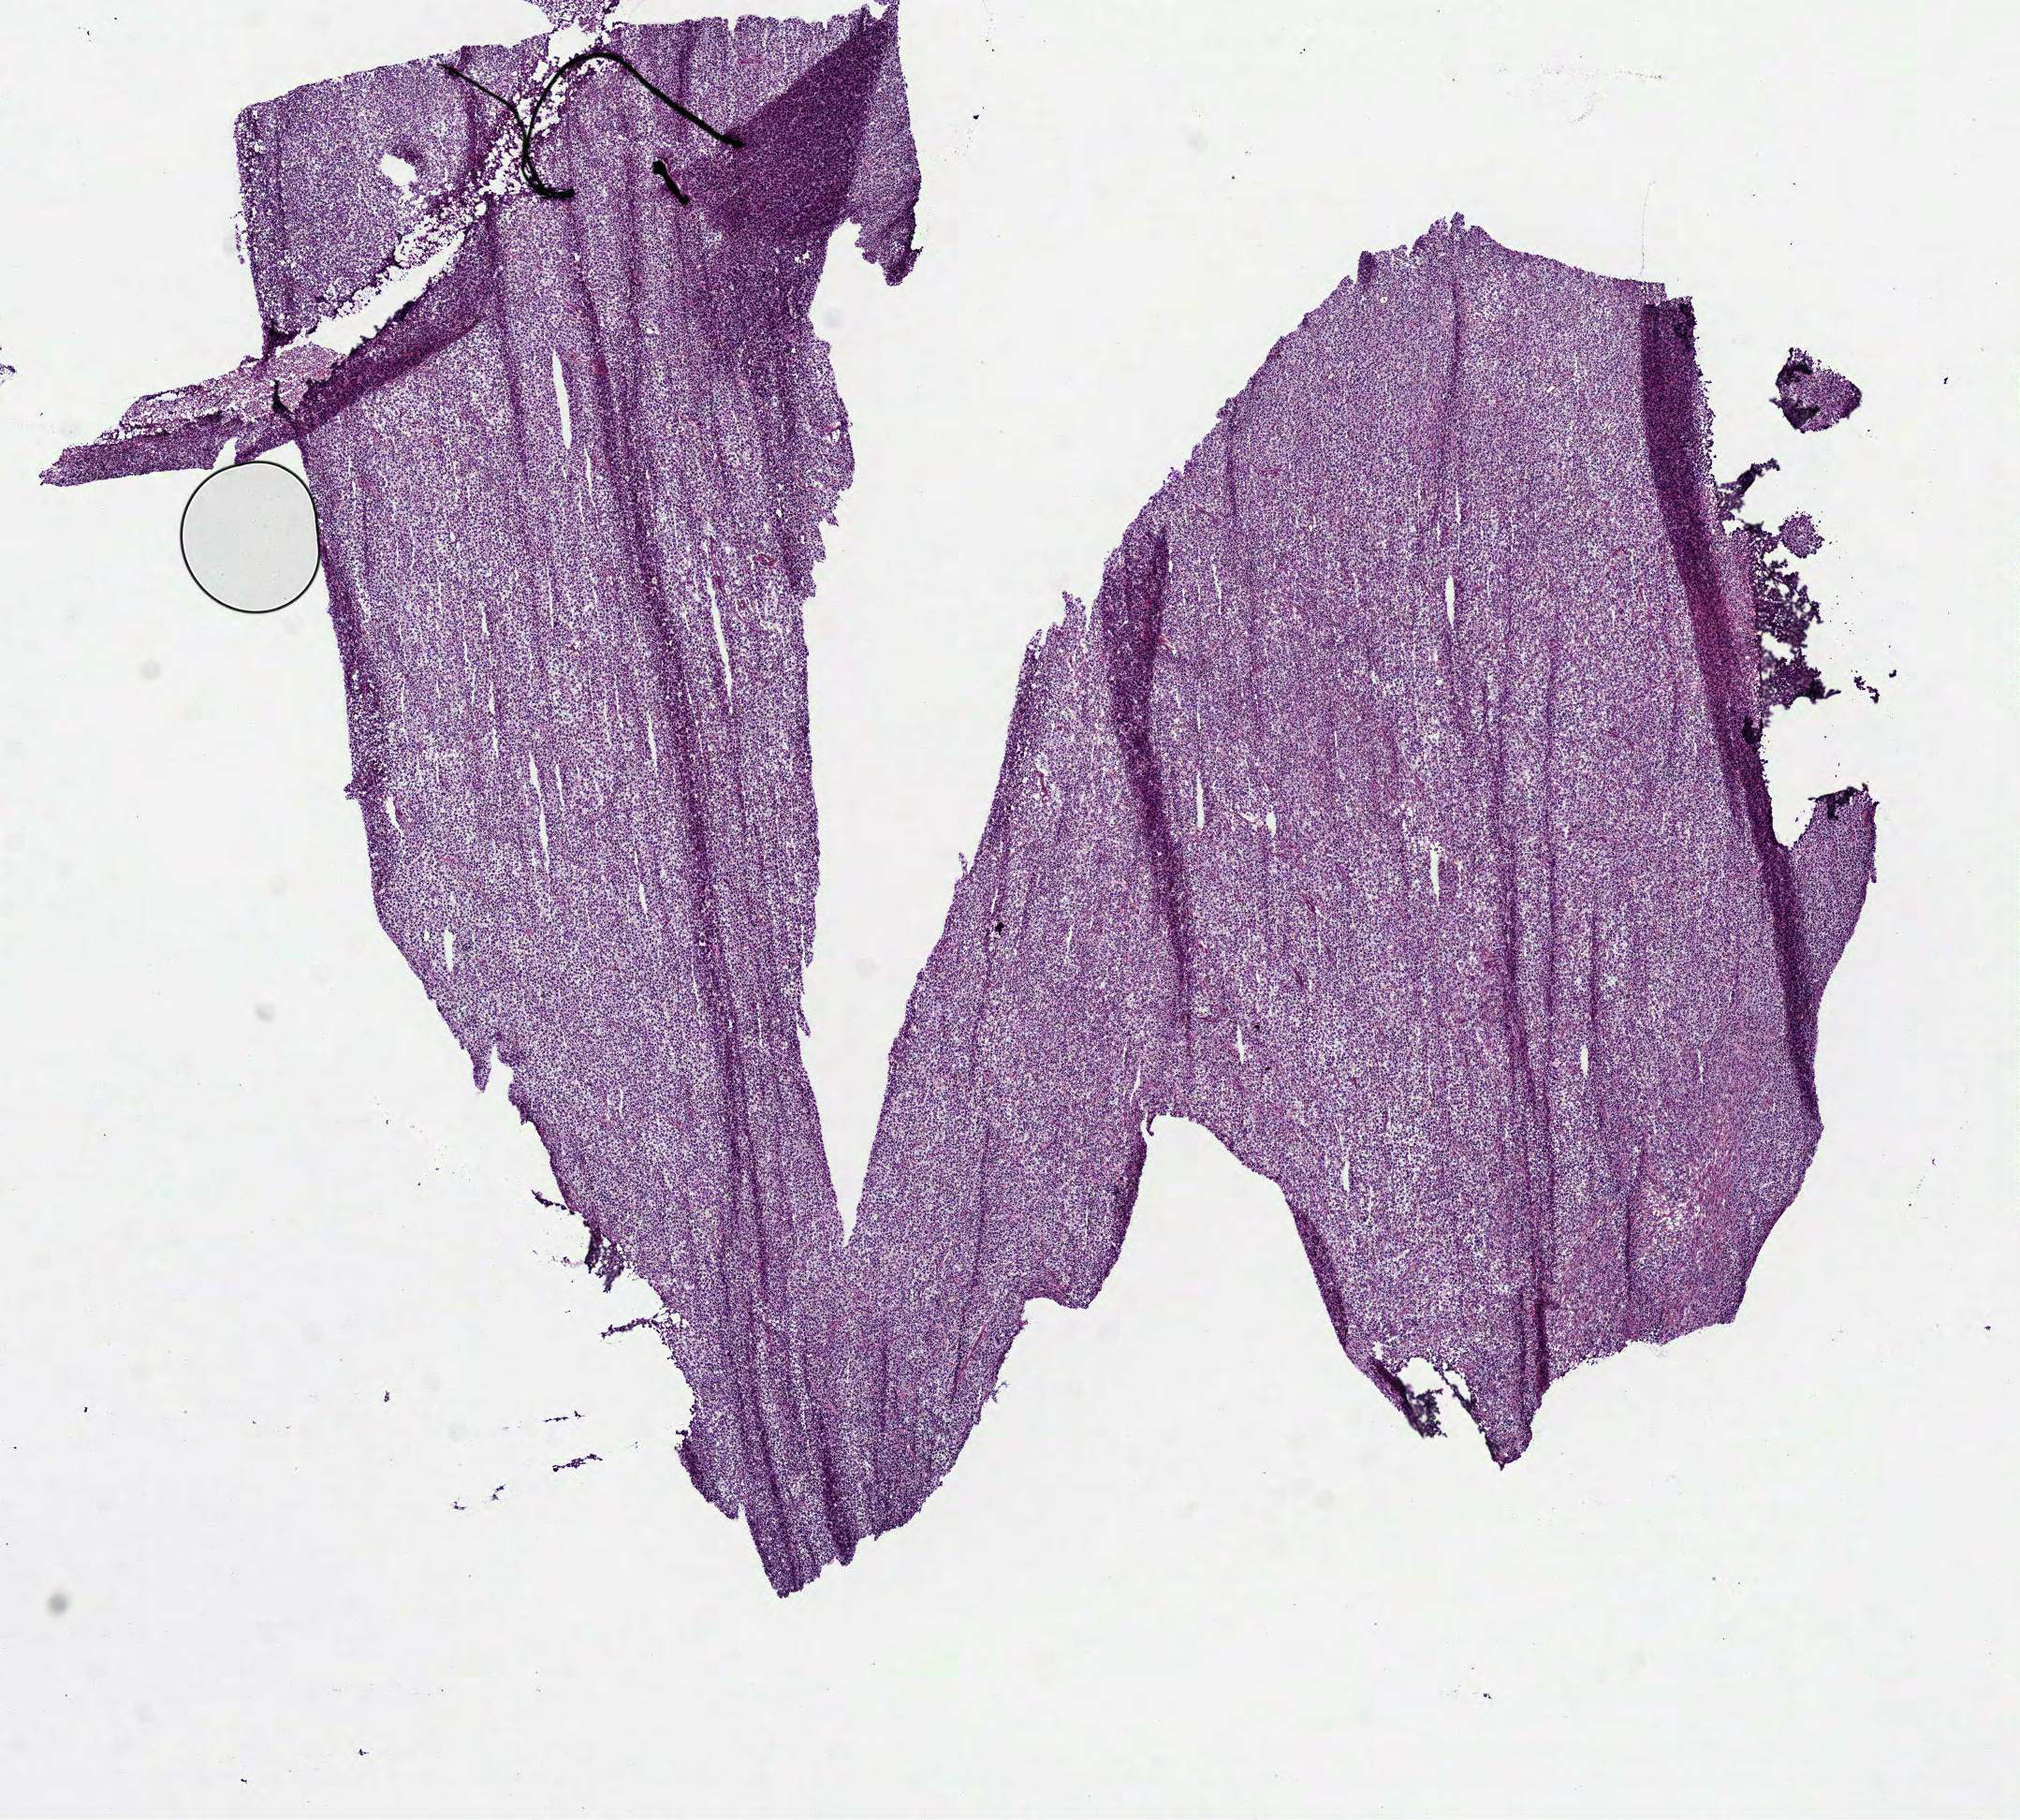
Hematoxylin and eosin (H&E) stained whole-slide image — whole scanned area (about 8.7 x 7.8 mm) shown as a low-resolution overview, frozen section, sample: primary tumour, lymphoid tissue. Patient: female, age at initial diagnosis 28 years. Slide review estimates, as recorded: tumour cells 100%, tumour nuclei 90%, normal cells 0%, stromal cells 0%, necrosis 0%. Infiltration values recorded for this section: lymphocyte infiltration 9%.
• pathologic diagnosis: Mediastinal (thymic) large B-cell lymphoma (anterior mediastinum)